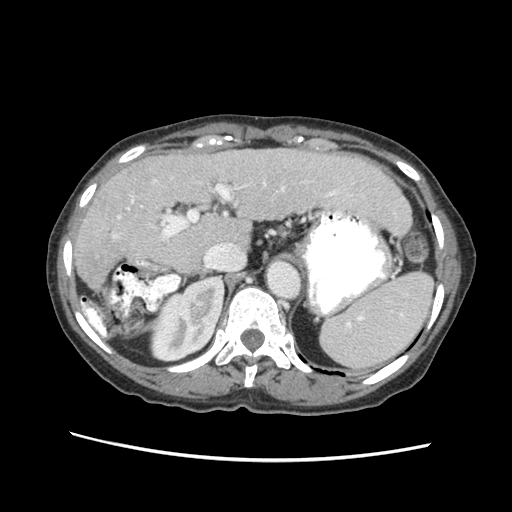
Contrast-enhanced abdominal CT (liver protocol), one axial slice. Slice 38 of 63 in the series (ordered by position). Soft-tissue window (W 400 / L 40 HU). 2.5 mm slice thickness. 512 × 512 image matrix. Case-level facts recorded for this patient, not image findings: diagnosis: hepatocellular carcinoma (patient treated with transarterial chemoembolisation; whether this scan precedes or follows treatment is not stated here); TNM stage (as recorded): Stage-I; Child-Pugh class: B; tumour differentiation: well differentiated.
Structures marked on this image (semi-automatic segmentation, software-assisted and operator-edited):
- abdominal aorta: bounding box [x1, y1, x2, y2] px = [267, 261, 298, 298]
- liver parenchyma outside the tumour (the mass and vessels are separate outlines, so this box may not span the whole liver): [74, 144, 410, 289]
- liver vessels: [130, 181, 334, 215]